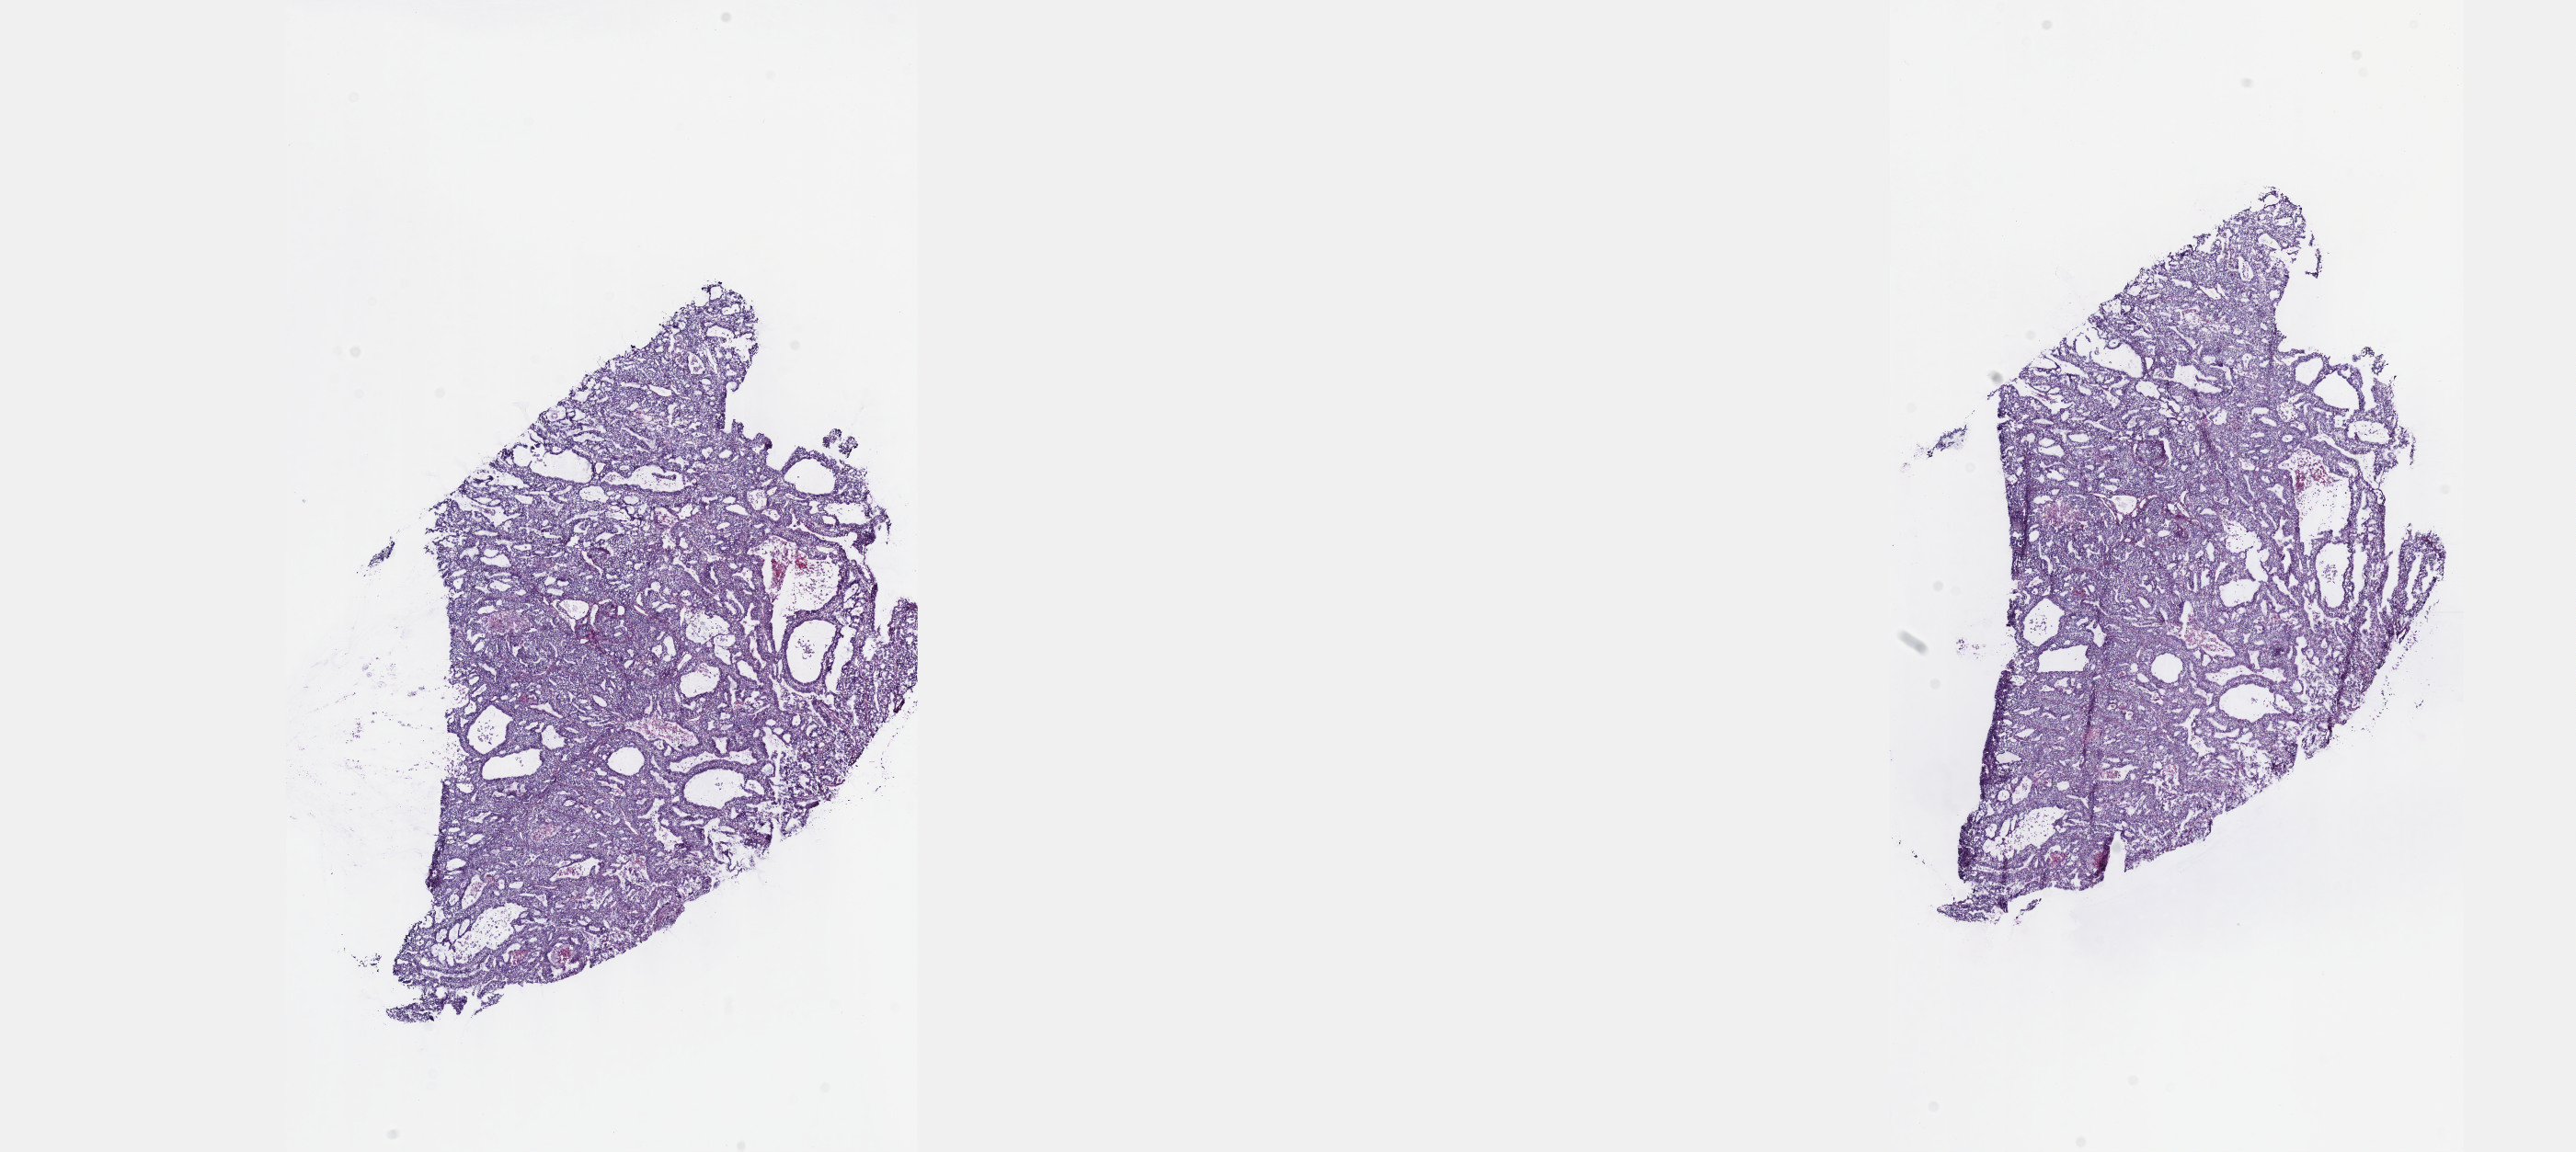
Whole-slide histology image, Hematoxylin and eosin (H&E) stained — shown as a low-resolution overview of the whole scanned area (about 22.6 x 10.1 mm); frozen section from the top of the tissue portion; primary tumour sample from the uterus. Female patient; age at initial diagnosis 70 years. Histologic grade: G2 (moderately differentiated). Slide review estimates, as recorded: tumour cells 60%, tumour nuclei 70%, normal cells 0%, stromal cells 30%, necrosis 10%. Inflammatory infiltration, as recorded: lymphocyte infiltration 0%, monocyte infiltration 0%, neutrophil infiltration 0%.
- pathologic diagnosis: Endometrioid adenocarcinoma, NOS (endometrium)
- FIGO stage: I